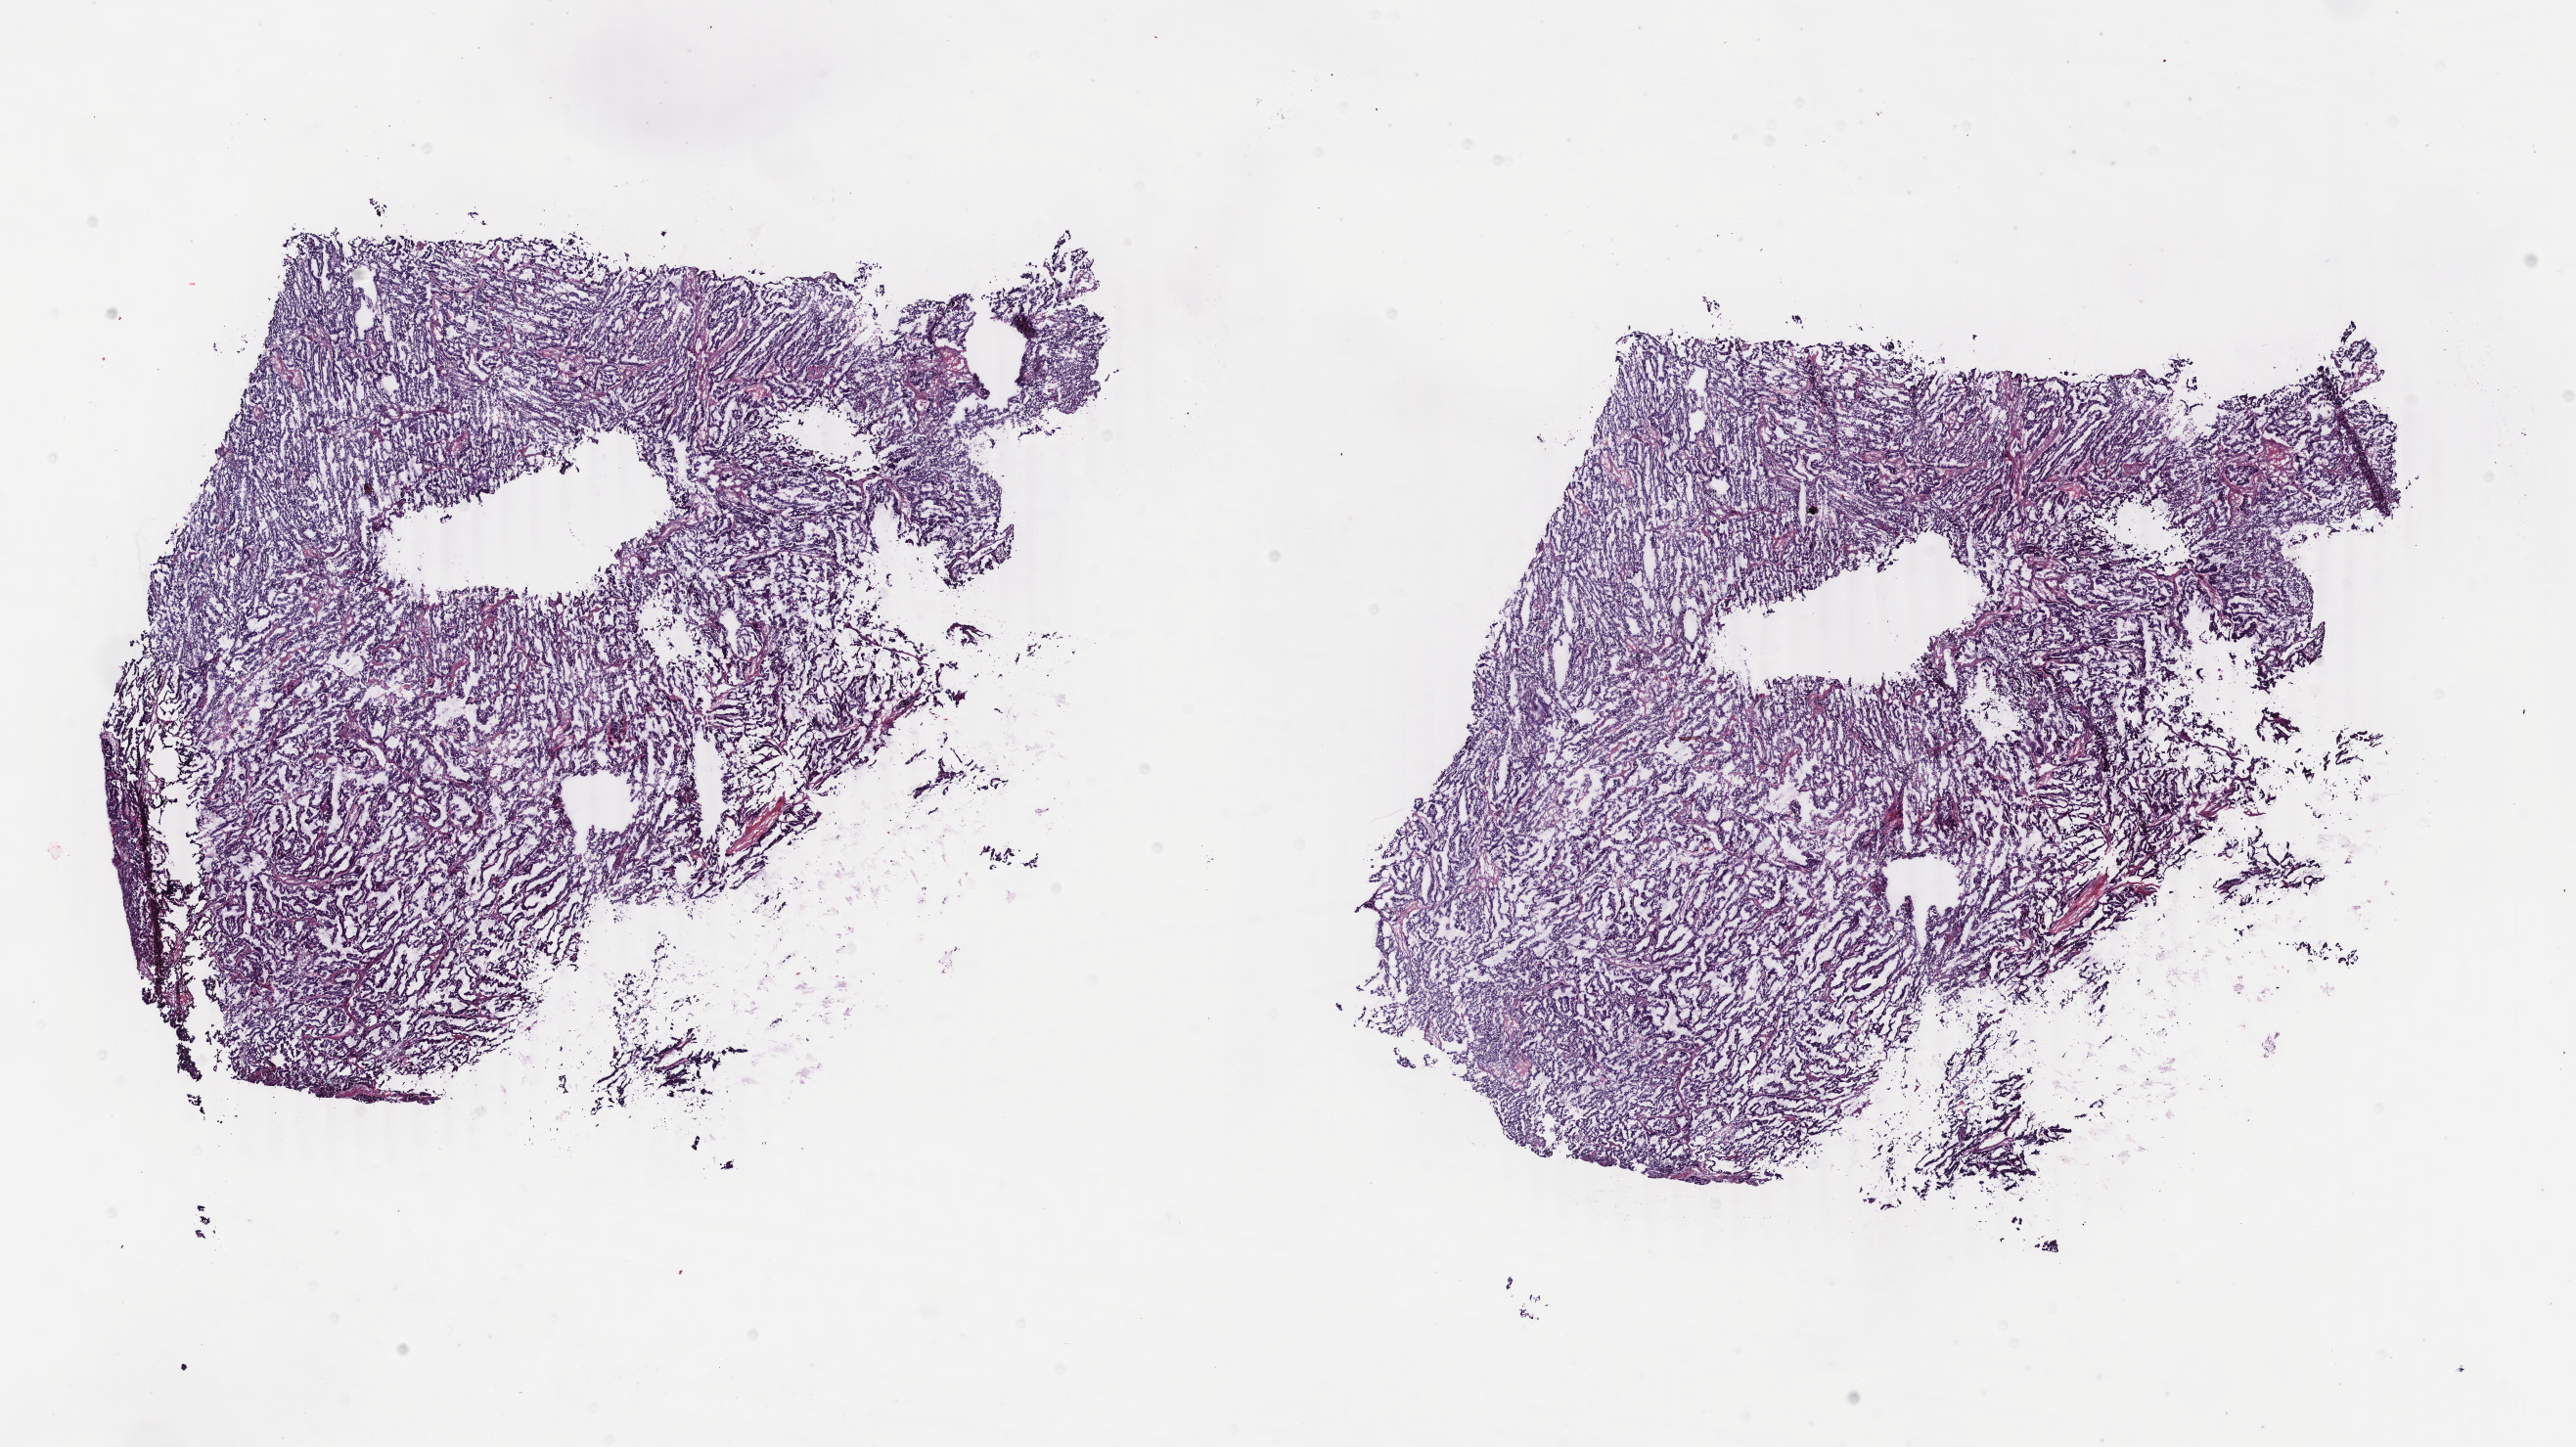
Digitized H&E tissue section (whole slide), low-resolution overview of the scanned area, about 20.9 x 11.8 mm; frozen section from the top of the tissue portion; sample: primary tumour, uterus. Patient: female, age at initial diagnosis 56 years. Histologic grade: G1 (well differentiated). Slide review estimates, as recorded: tumour cells 100%, tumour nuclei 95%, normal cells 0%, stromal cells 0%, necrosis 0%. Infiltration values recorded for this section: lymphocyte infiltration 0%, monocyte infiltration 0%, neutrophil infiltration 0%.
- FIGO stage: IA
- lymph nodes positive (case pathology): 0 of 8 examined
- histologic diagnosis: Endometrioid adenocarcinoma, NOS (endometrium)